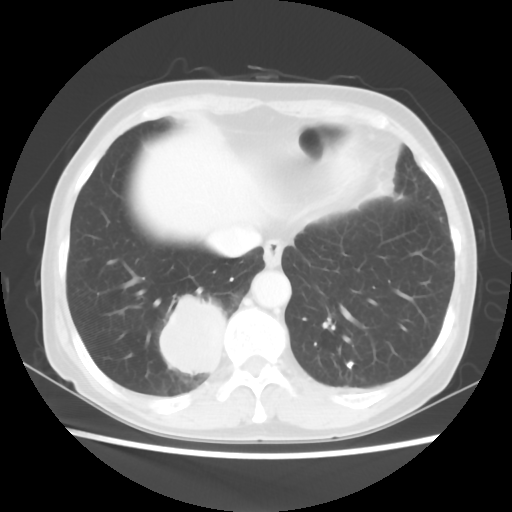
Chest CT, one axial slice. Position 14 of 56 along the scan axis. Reconstruction kernel STANDARD. 120 kVp. Lung window (W 1500 / L -600 HU). 5 mm slice thickness. 512 × 512 image matrix. Patient: female, 66 years. From the clinical record (not read from this slice): clinical TNM (as recorded): T2 N3 M0; histopathological grade: G3.
Outlined on this slice (bounding box drawn by a radiologist):
- lung tumour (recorded histology: small cell carcinoma): bounding box [x1, y1, x2, y2] px = [151, 285, 241, 383]